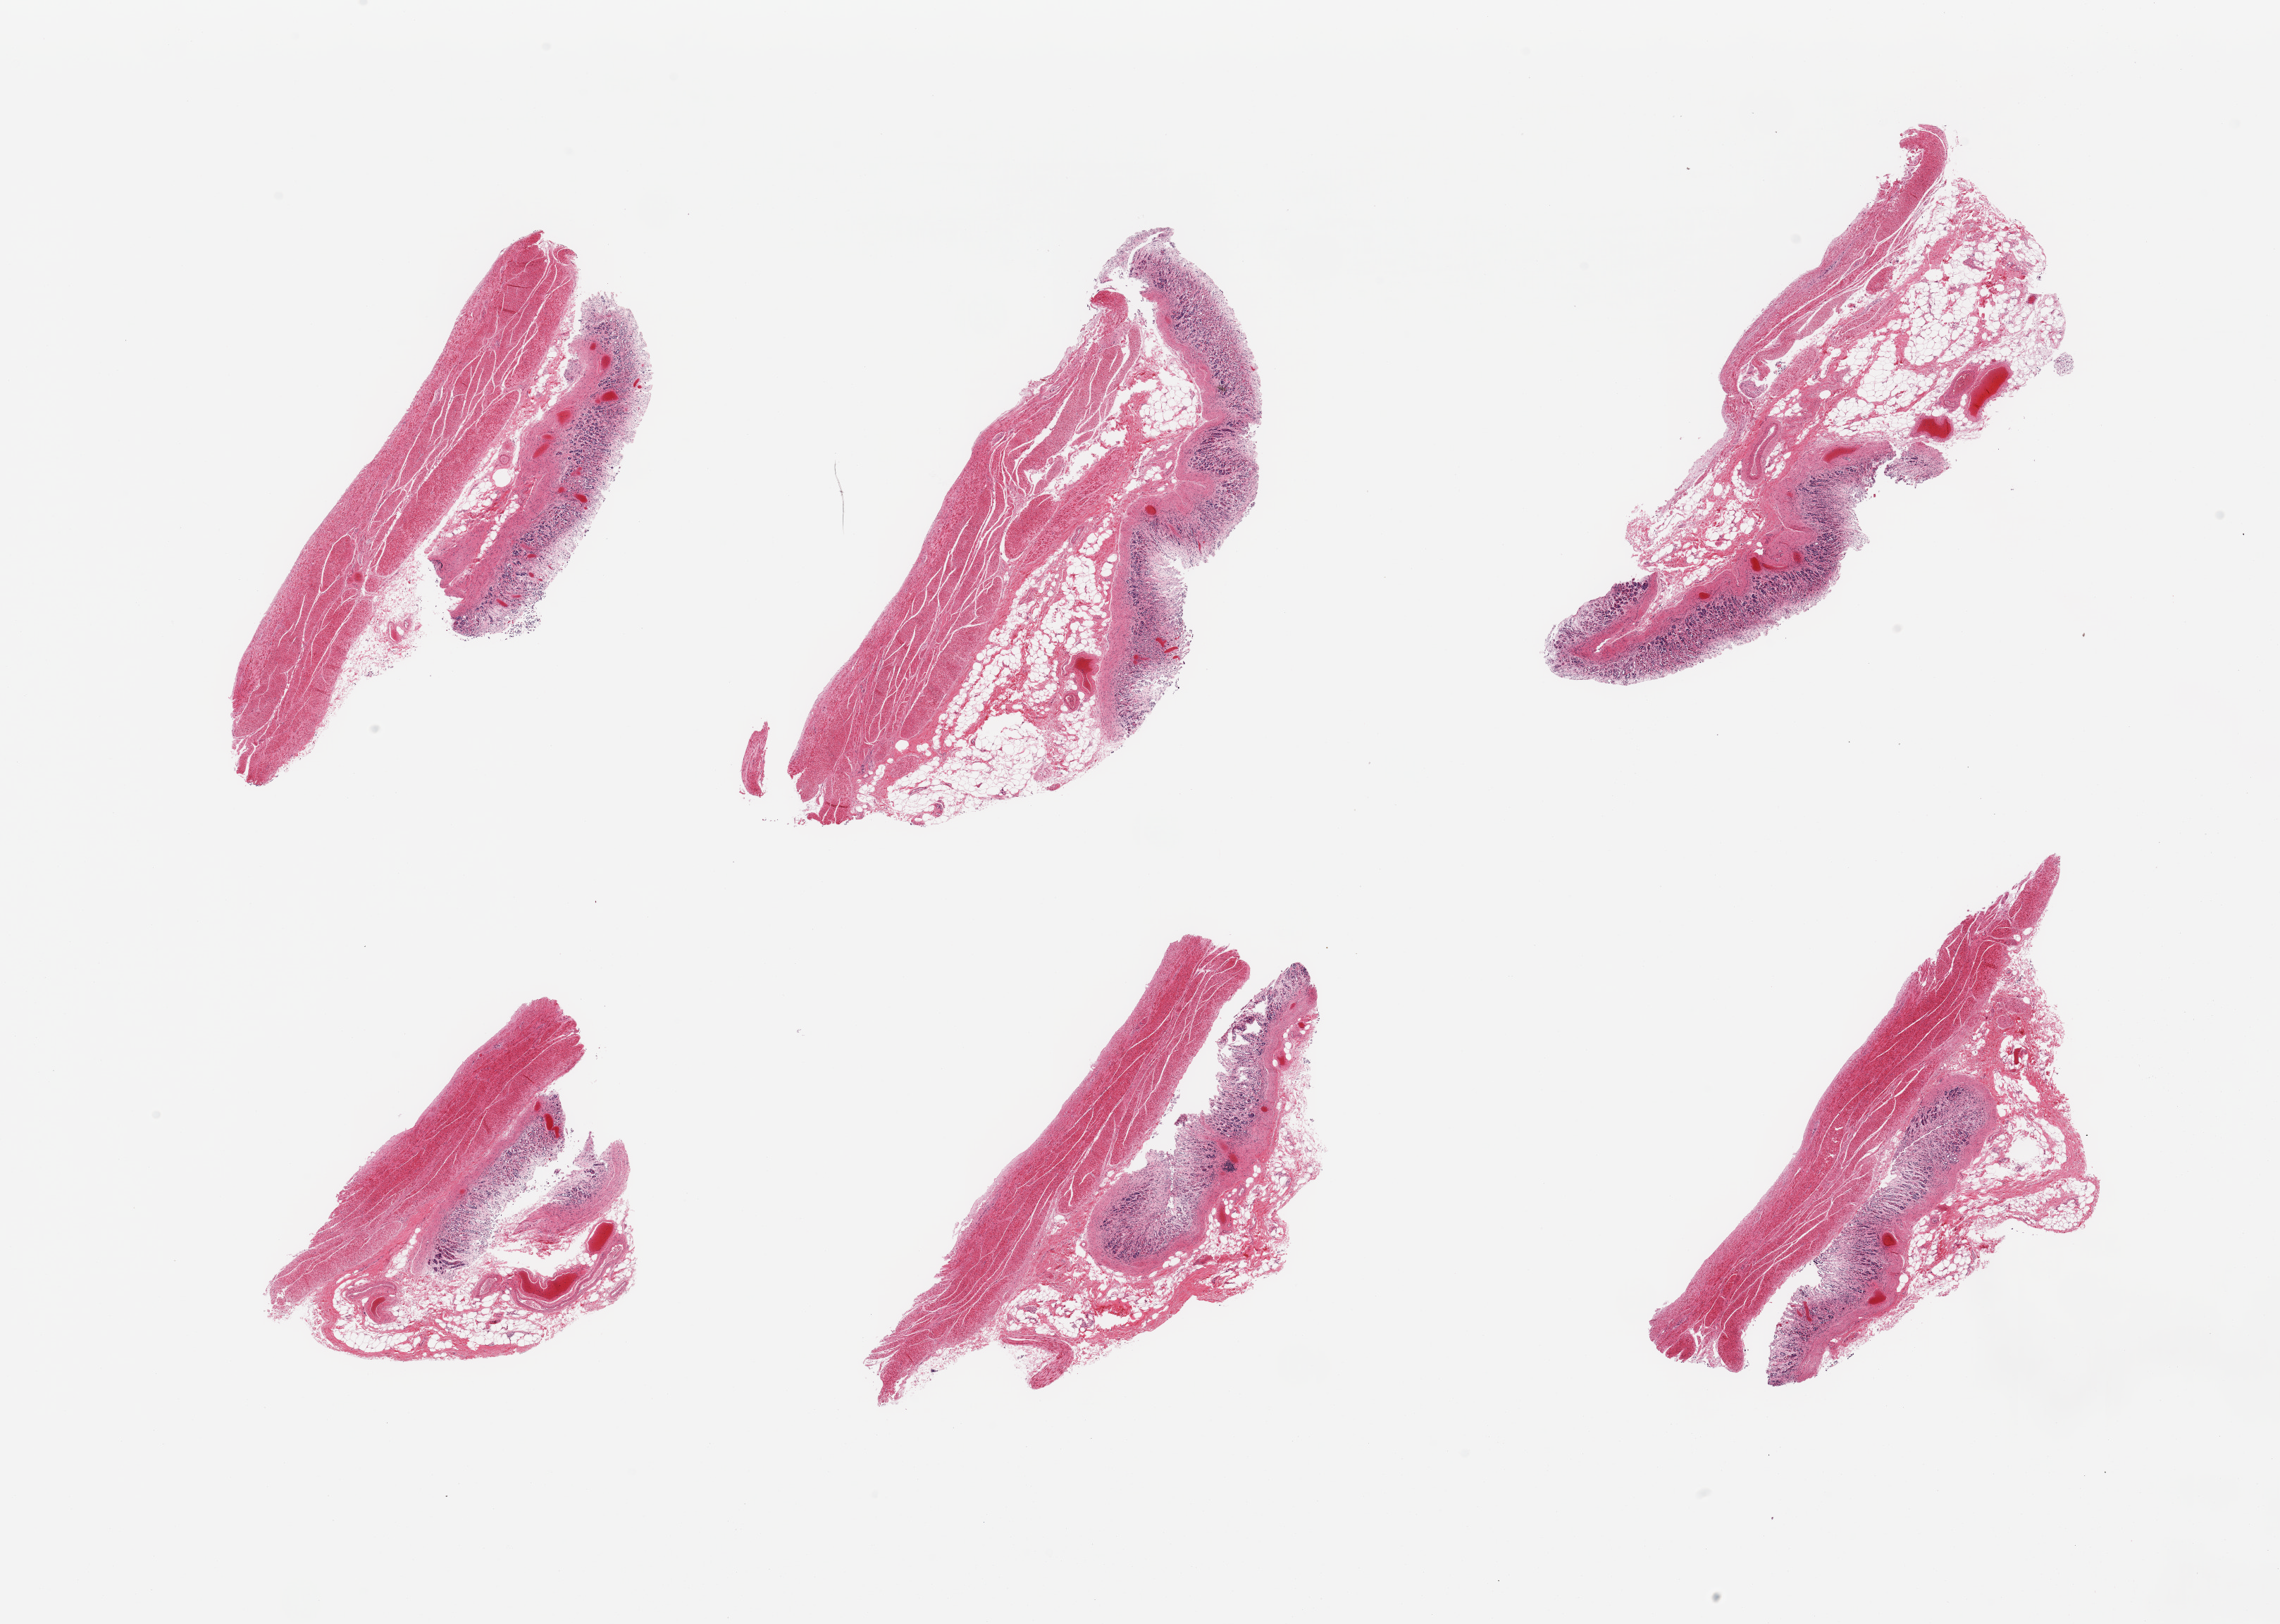
Whole-slide image, H&E stain — low-resolution overview of the scanned area, about 25.6 x 18.2 mm (slide scanned at 20x). PAXgene-fixed paraffin-embedded (PFPE) section. Target tissue: stomach. Tissue donor sample. Donor sex: male.
* reviewer comment on this tissue sample: 6 pieces; mucosa largely autolyzed; muscularis moderately autolyzed